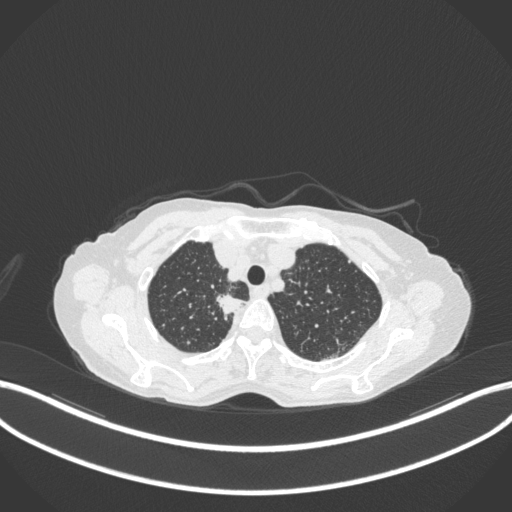
Chest CT, one axial slice. Slice 313 of 363 in the series (ordered by position). Reconstruction kernel B31f. 120 kVp. Lung window (W 1500 / L -600 HU). 512 × 512 image matrix, field of view 400 × 400 mm. Female patient, age 75 years. From the clinical record (not read from this slice): clinical TNM (as recorded): T1c N1 M1.
Outlined on this slice (rectangle marked by the reading radiologist):
- lung tumour (recorded histology: adenocarcinoma): bounding box [x1, y1, x2, y2] px = [214, 287, 246, 320]